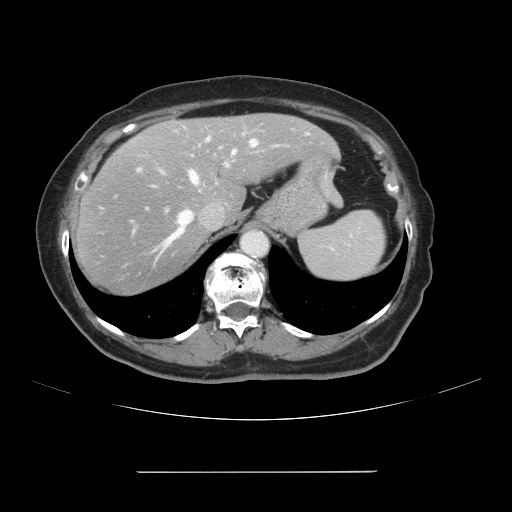
Contrast-enhanced abdominal CT, one axial slice; slice 80 of 111 in the series (ordered by position); 120 kVp; soft-tissue window (W 400 / L 40 HU); 512 × 512 image matrix. Female patient, age 74 years. From the clinical record (not read from this slice): diagnosis: colorectal cancer liver metastases, imaged before liver resection; multiple liver metastases: yes; largest metastasis: 1.1 cm; disease in both lobes: yes.
Structures marked on this image (manually delineated by an expert):
- hepatic veins: bounding box [x1, y1, x2, y2] px = [149, 138, 257, 262]
- liver: [73, 114, 335, 295]
- planned liver remnant (the part of the liver to remain after resection): [159, 114, 335, 220]
- portal vein (with intrahepatic branches): [139, 137, 228, 171]